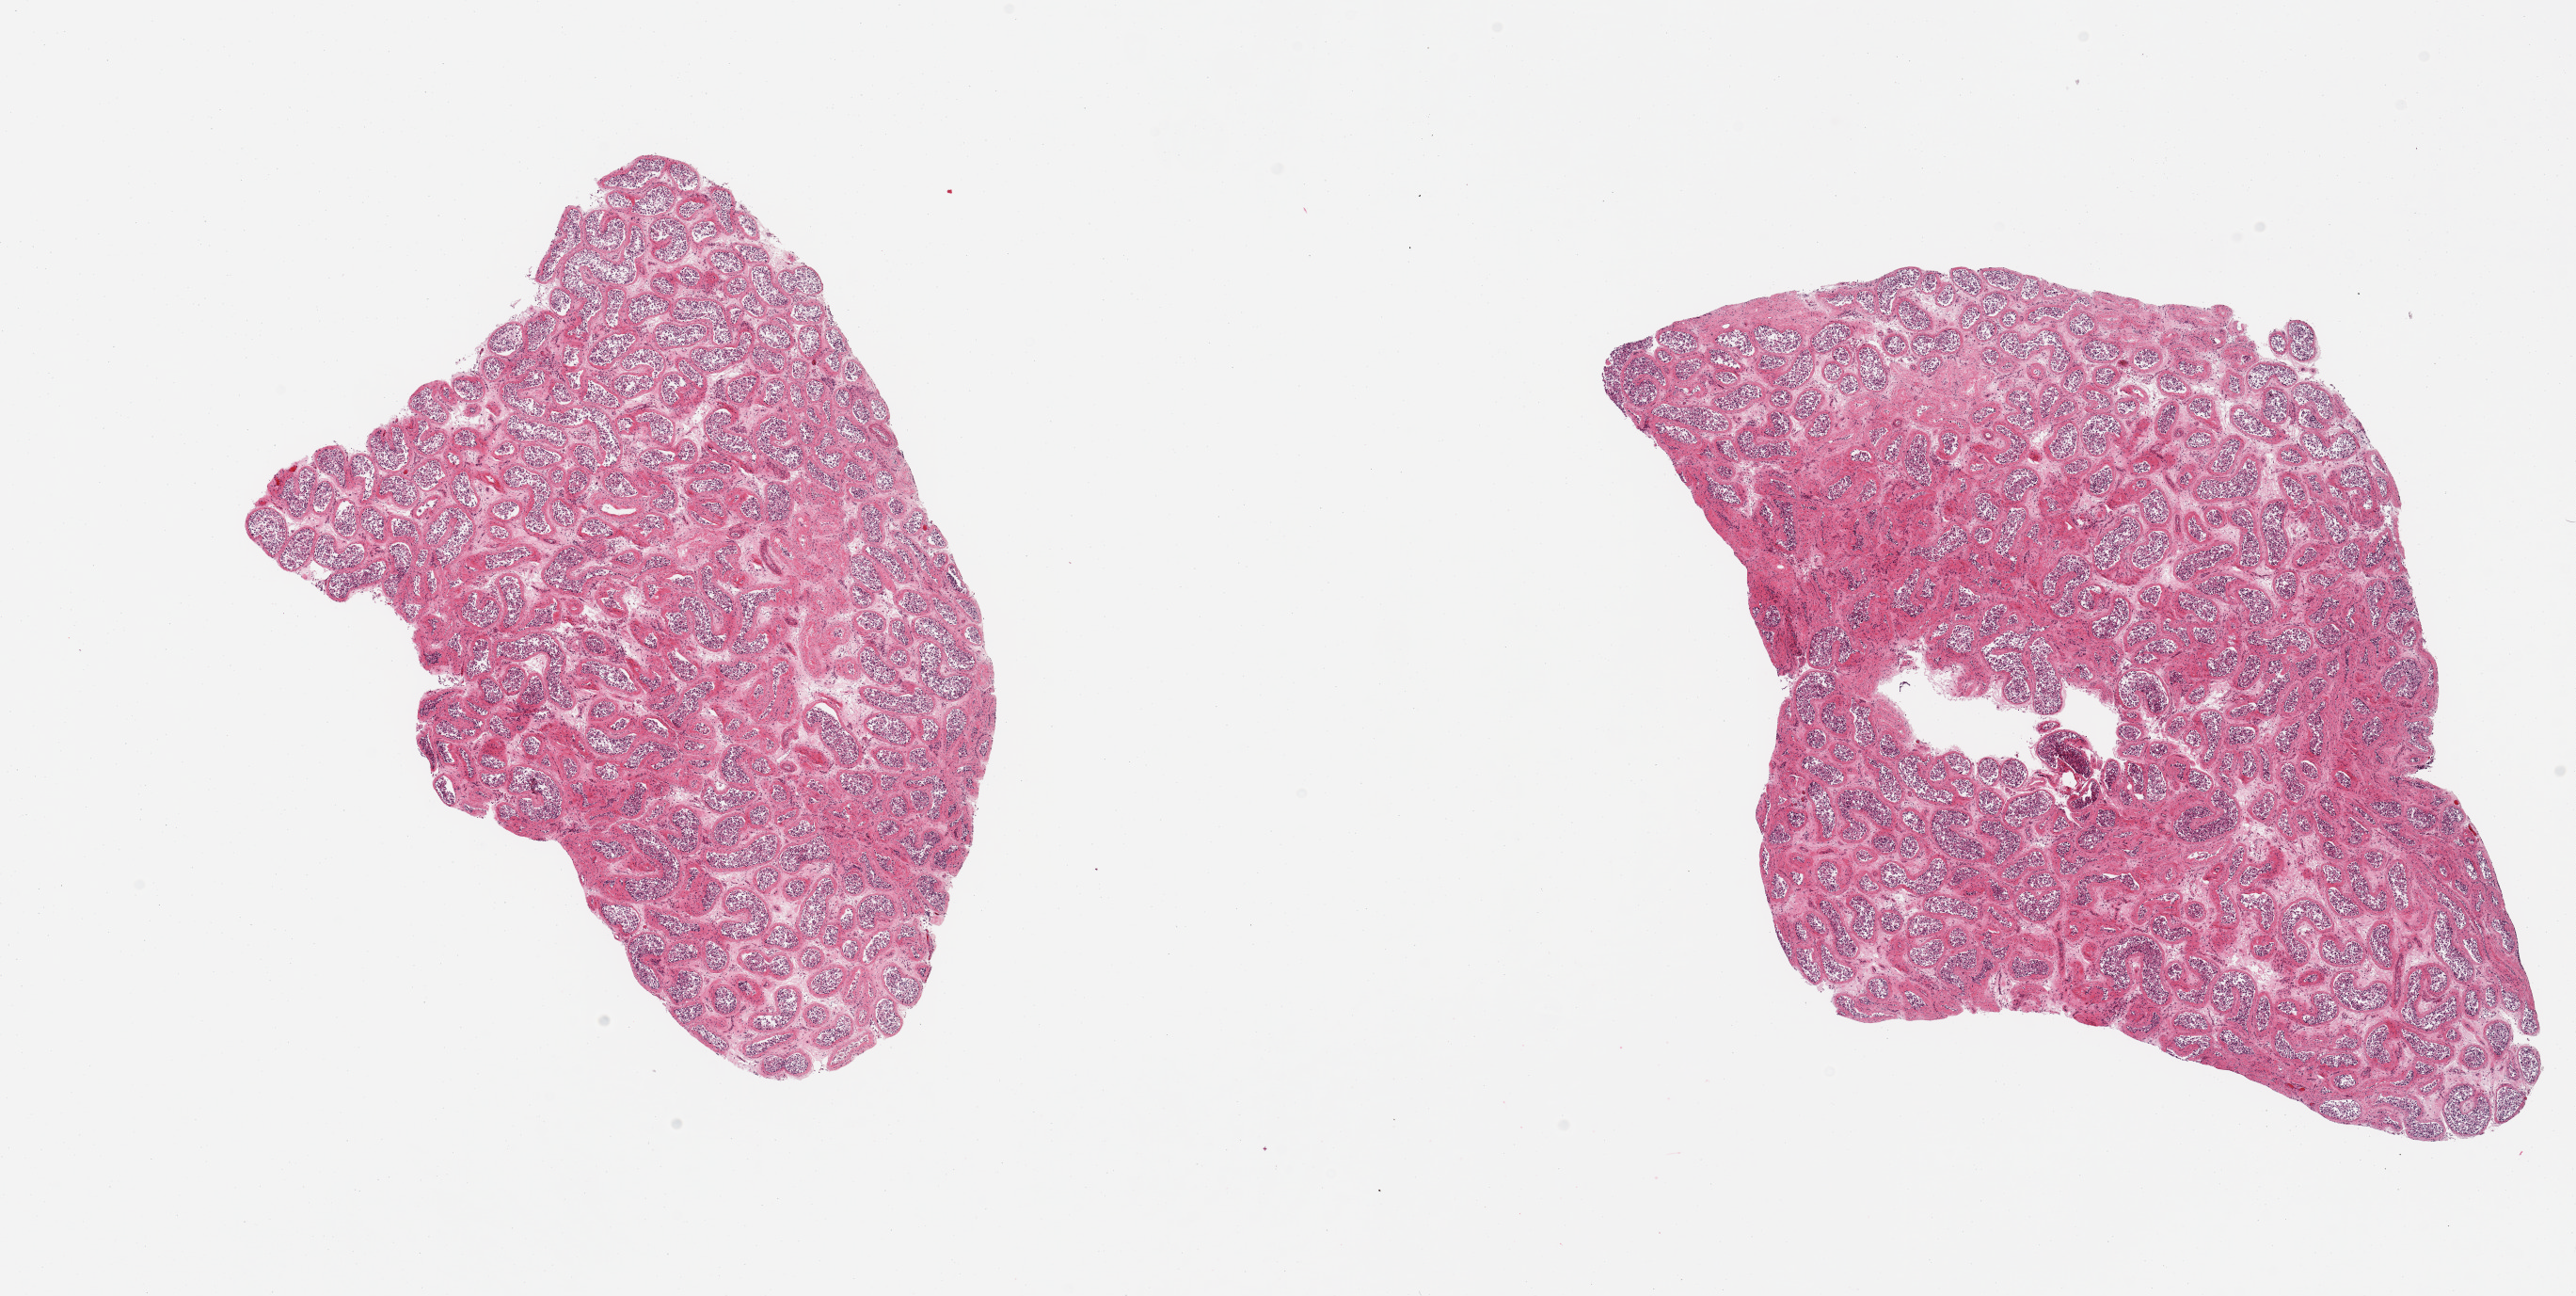
Whole-slide image, hematoxylin and eosin (H&E) stain, a low-resolution overview of the entire scanned area, about 21.7 x 10.9 mm (from a 20x scan). PAXgene-fixed, paraffin-embedded tissue. Target tissue: testis. Donor tissue sample.
Review note (as recorded): 2 pieces, reduced spermatogenesis, patchy tubular atrophy/hyalinization.